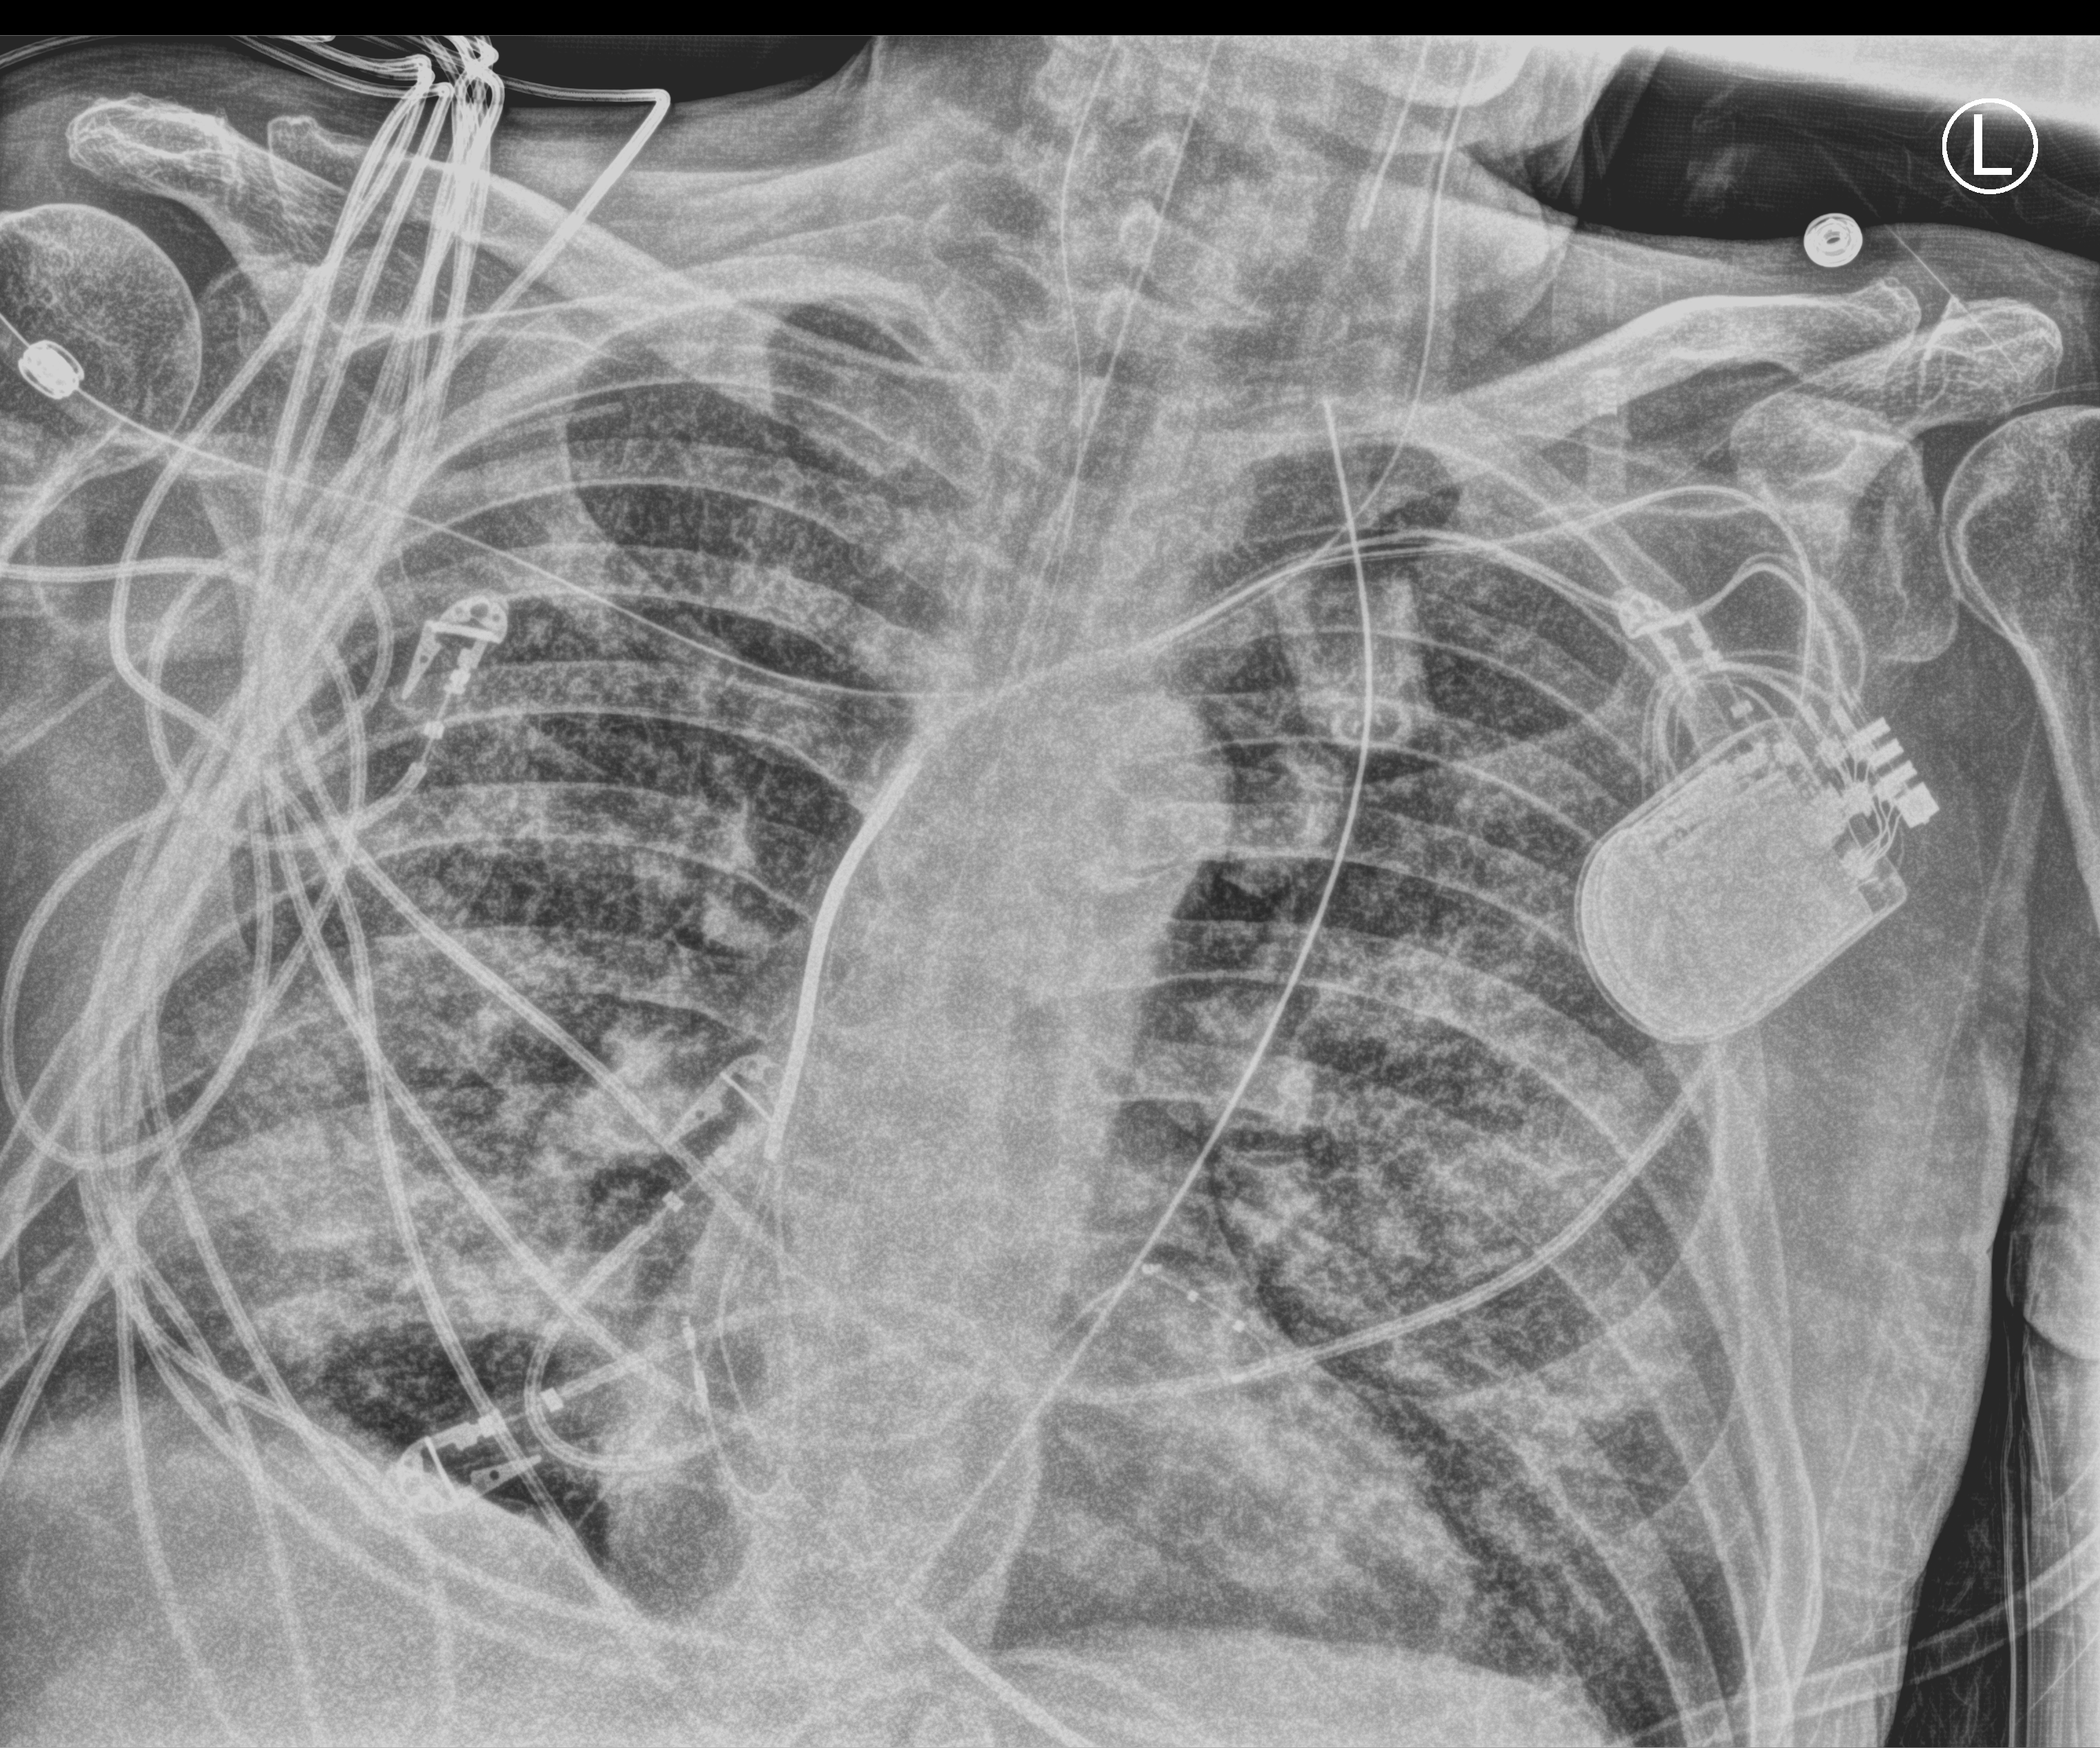
Chest X-ray (portable), anteroposterior (AP) projection. Patient hospitalised with COVID-19; male, aged 60–74 years.
From the hospital-stay record, not from the radiograph (when in the stay this image was taken is not recorded): admitted to intensive care during this hospital stay: yes.